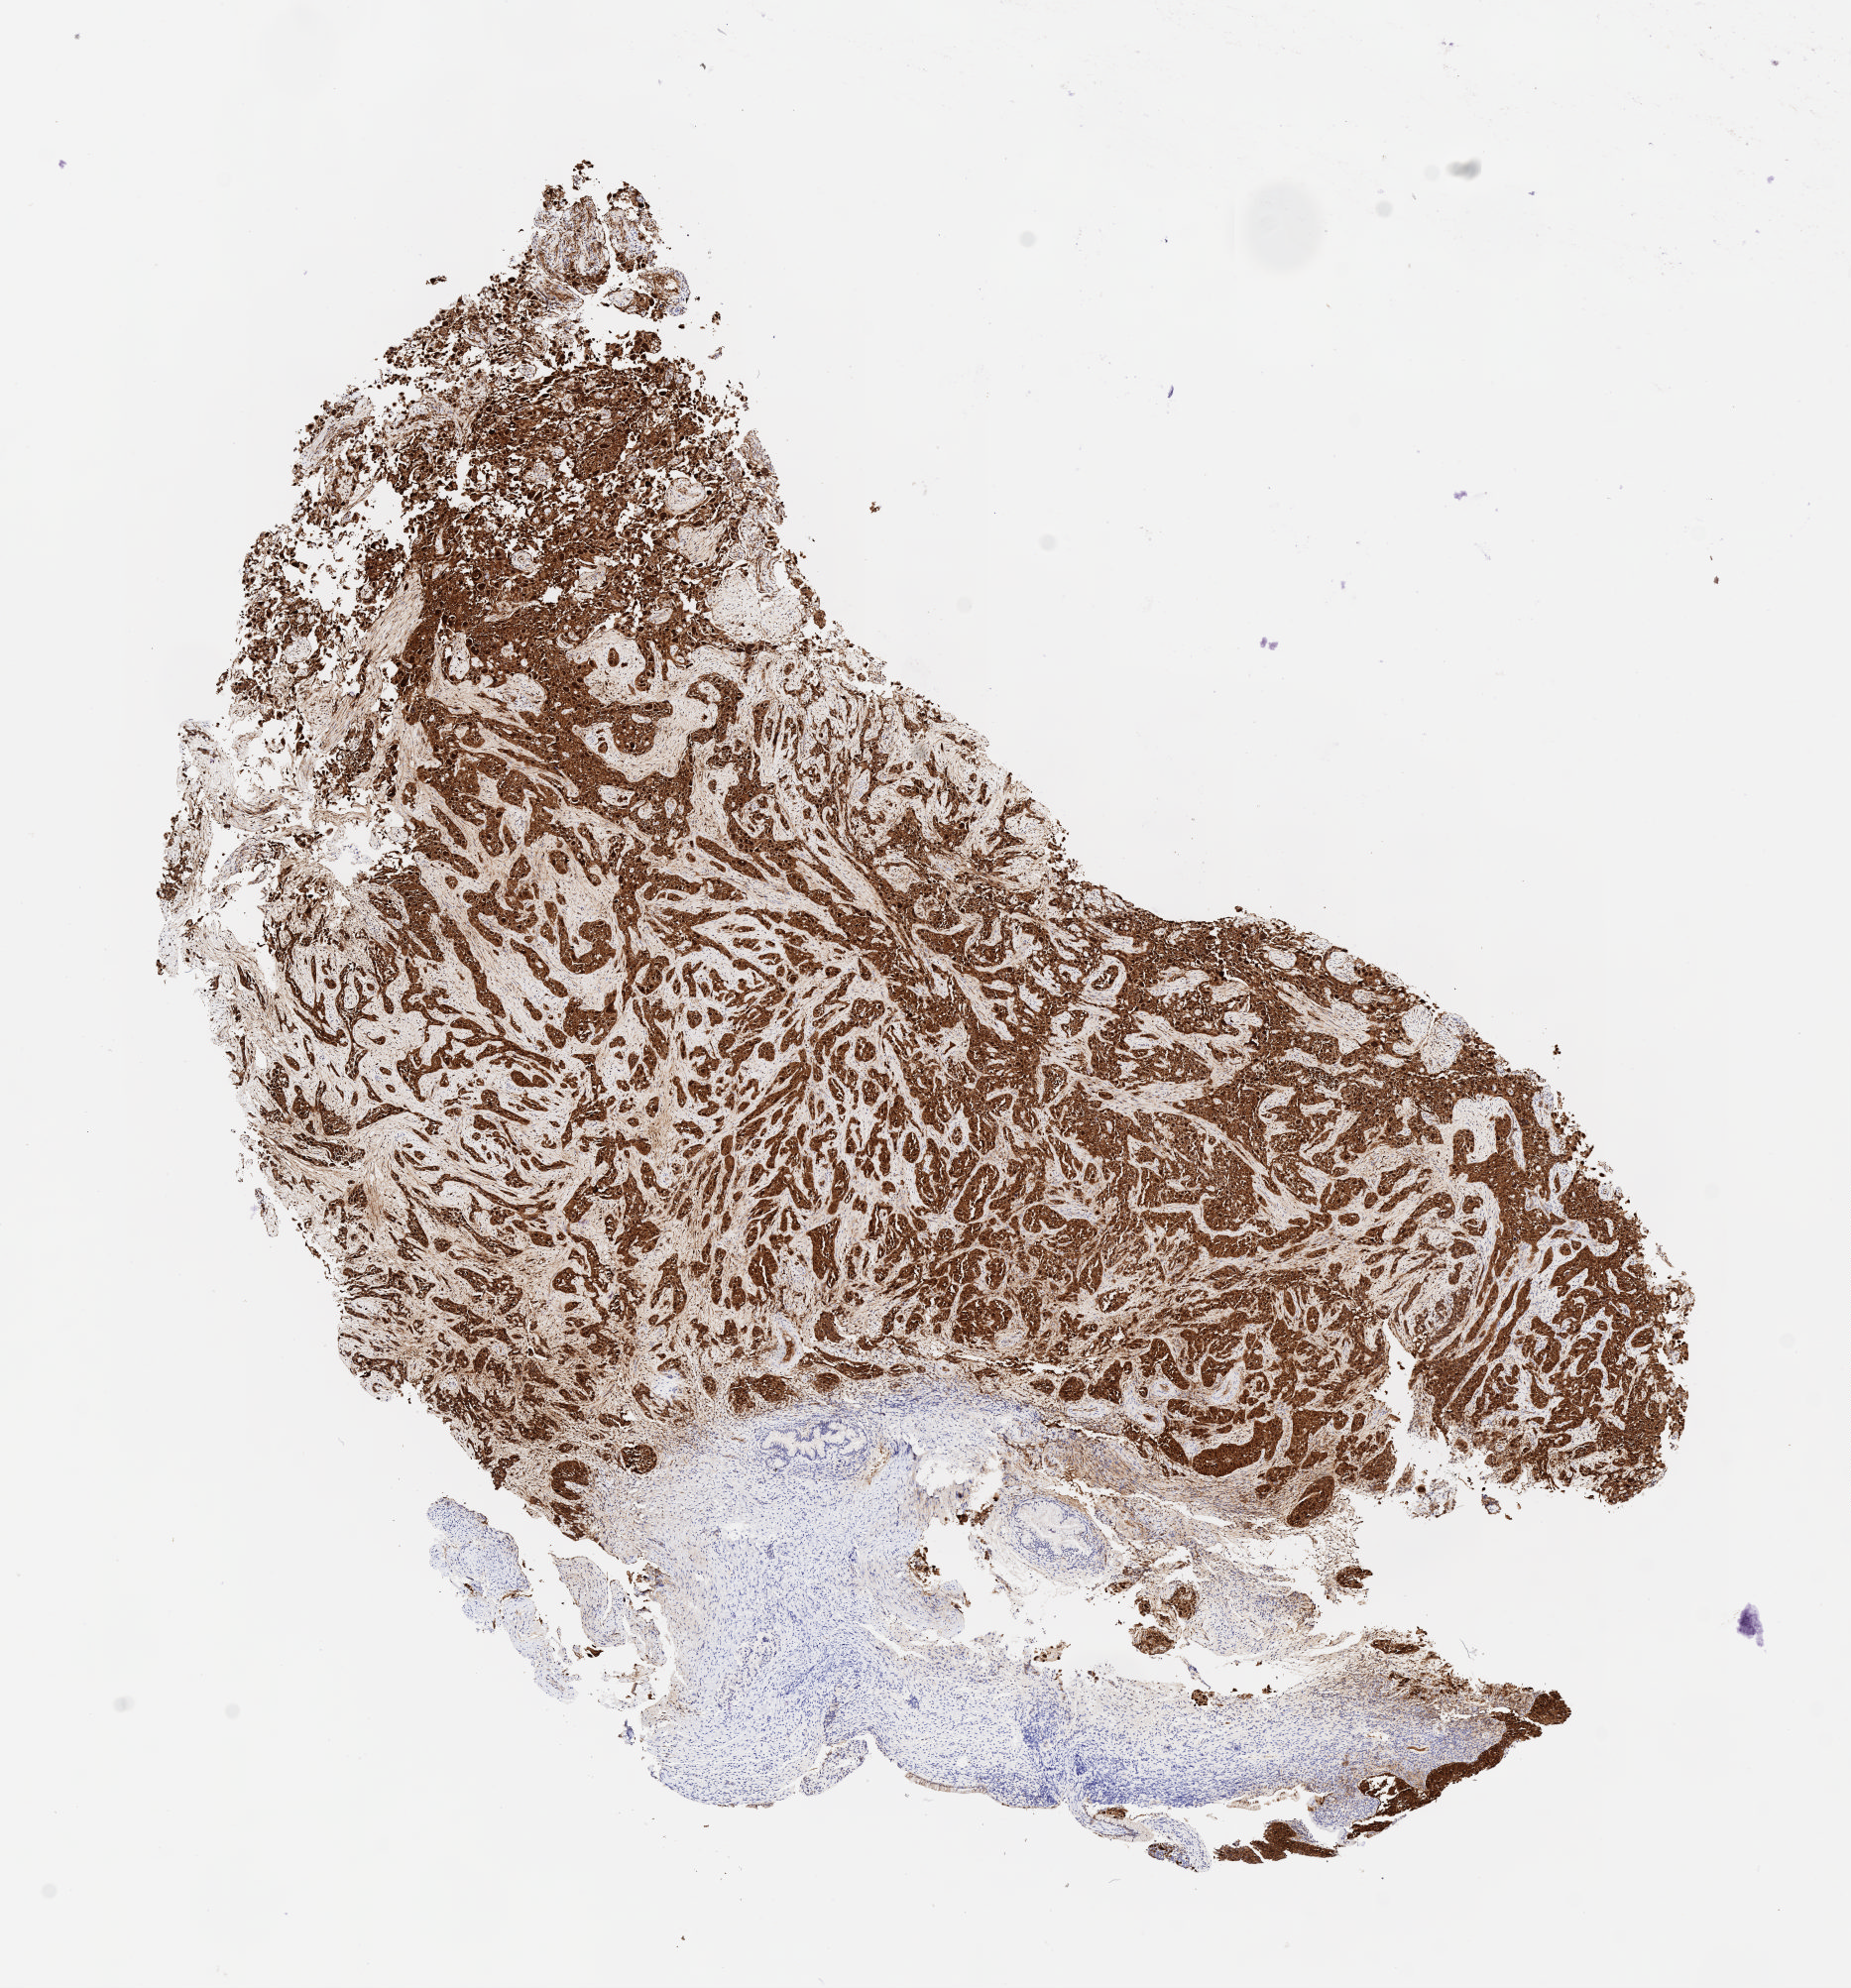
Whole-slide image, immunohistochemical stain for p16 (p16INK4a) — shown as a low-resolution overview of the whole scanned area (about 7.5 x 8.1 mm). Tumor tissue. Anatomic site: cervix. Patient: female, aged 38.
Diagnosis: Squamous cell carcinoma, large cell, nonkeratinizing, NOS.